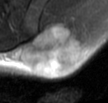
MRI of an extremity soft-tissue mass, one axial slice; position 24 of 42 along the scan axis; T2-weighted fat-saturated; MR volume resampled by the dataset authors to the PET/CT grid (not the native acquisition matrix); 3.27 mm slice thickness; 108 × 103 image matrix, field of view 105 × 101 mm. Male patient. Case-level facts recorded for this patient, not image findings: histological type: leiomyosarcoma; grade: intermediate; site of the primary tumour: left pelvis.
Structures marked on this image (expert contour drawn on MRI and transferred to this co-registered scan by the dataset authors):
- gross tumour volume (mass): bounding box <21,21,86,75> (left, top, right, bottom; pixels)